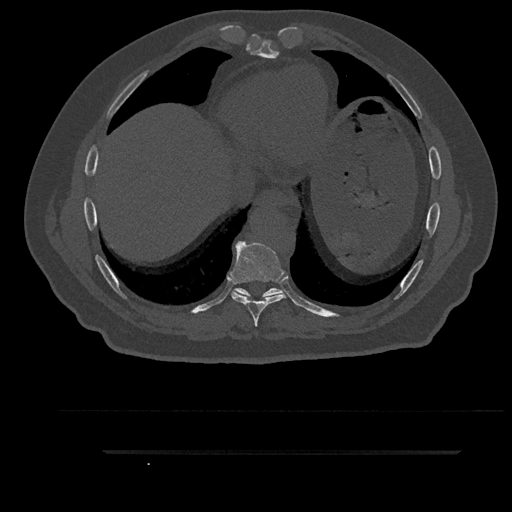
CT including the spine, one axial slice; slice 458 of 797 in the series (ordered by position); reconstruction kernel Br40s/3; 120 kVp; bone window (W 1800 / L 400 HU); 512 × 512 image matrix, field of view 432 × 432 mm. Male patient, age 63 years. Case-level facts recorded for this patient, not image findings: primary cancer: renal; vertebrae with lytic lesions (as recorded): T8.
Outlined on this slice (semi-automatically segmented with operator editing):
- T8 vertebra: bounding box [x1, y1, x2, y2] px = [231, 241, 286, 326]
- T9 vertebra: [234, 288, 283, 298]